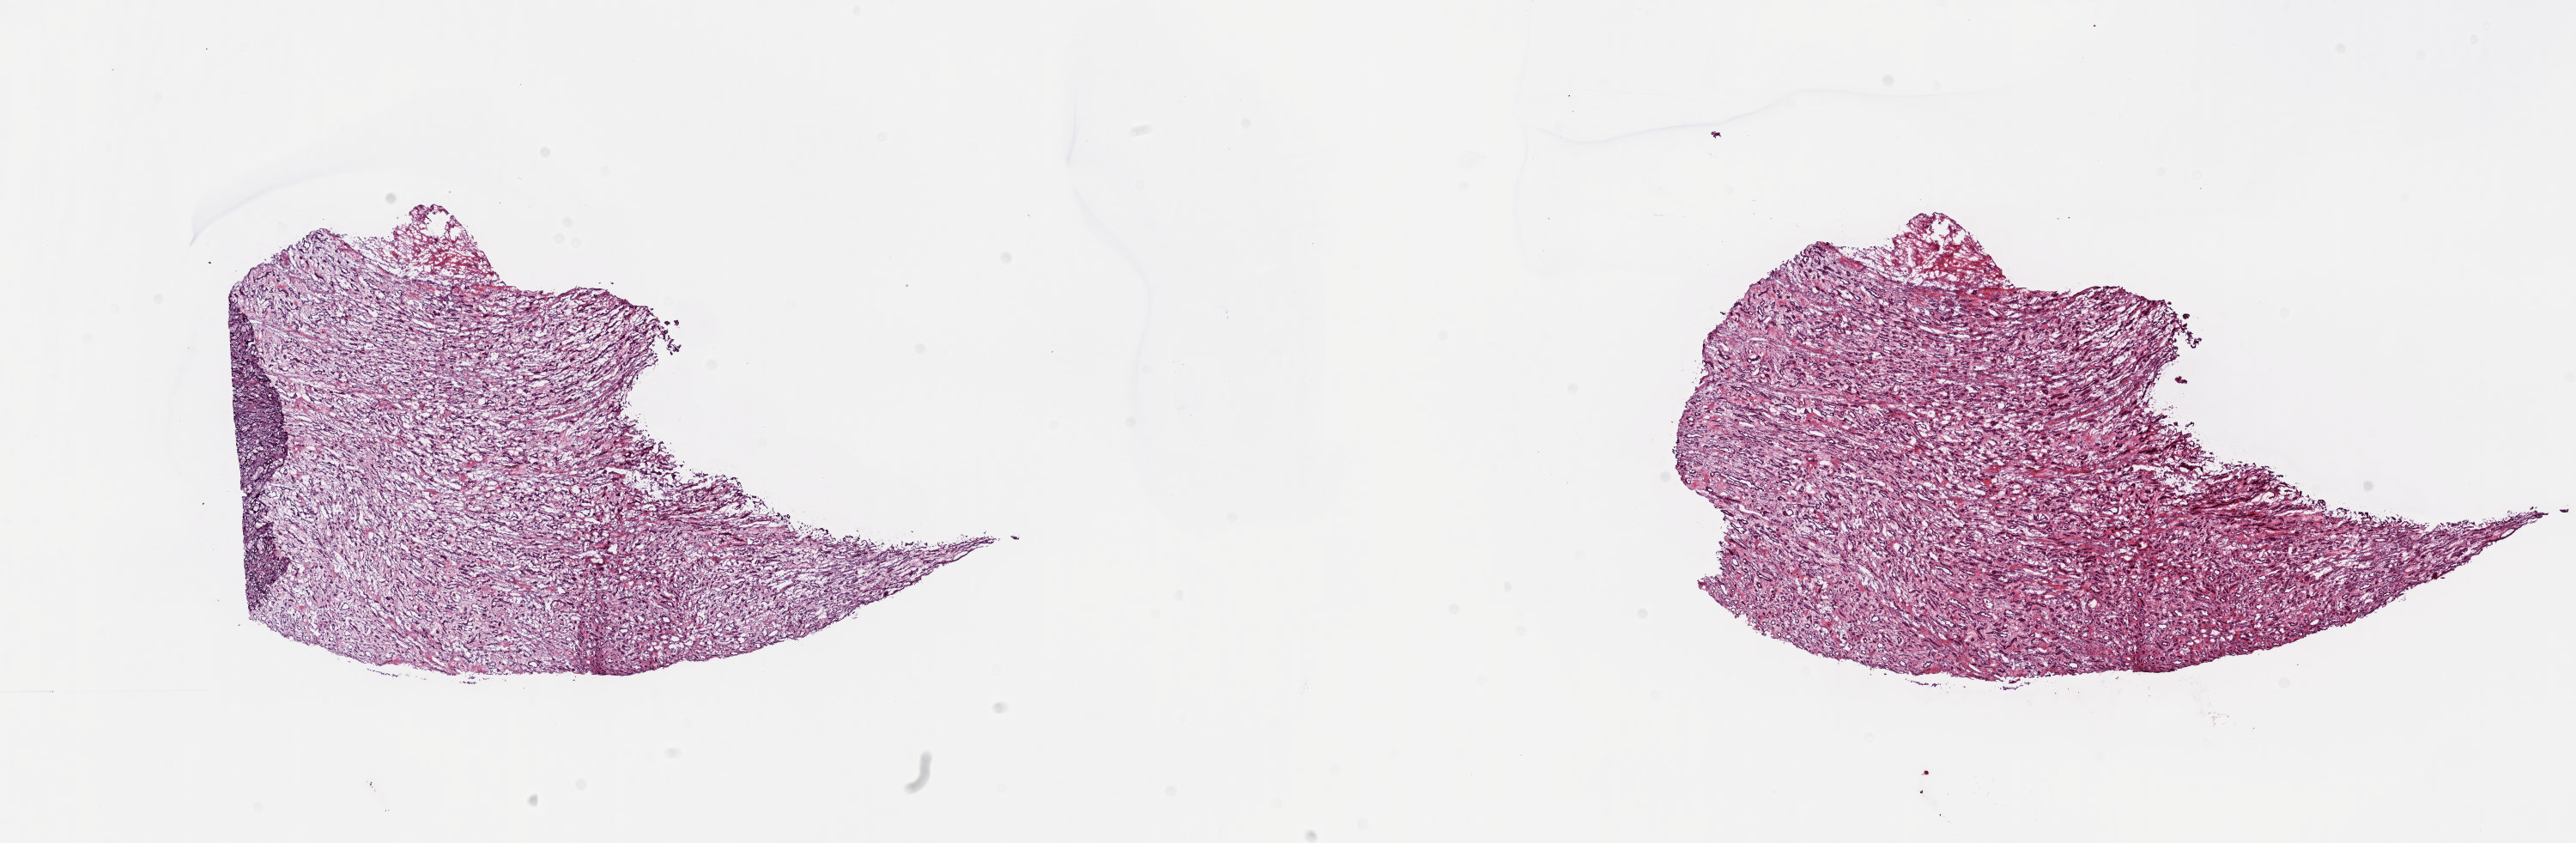
Whole-slide histology image, Hematoxylin and eosin (H&E) stained — low-resolution overview of the scanned area, about 23.8 x 7.8 mm. Frozen section. Solid tissue normal (non-tumour tissue) sample from the kidney. Male, age 63 years at initial diagnosis. Slide review estimates, as recorded: tumour cells 0%, tumour nuclei 0%, normal cells 35%, stromal cells 65%, necrosis 0%. Inflammatory infiltration, as recorded: lymphocyte infiltration 10%, monocyte infiltration 1%, neutrophil infiltration 1%.
• this section: solid tissue normal sample (biorepository sample class)
• patient diagnosis: Papillary adenocarcinoma, NOS